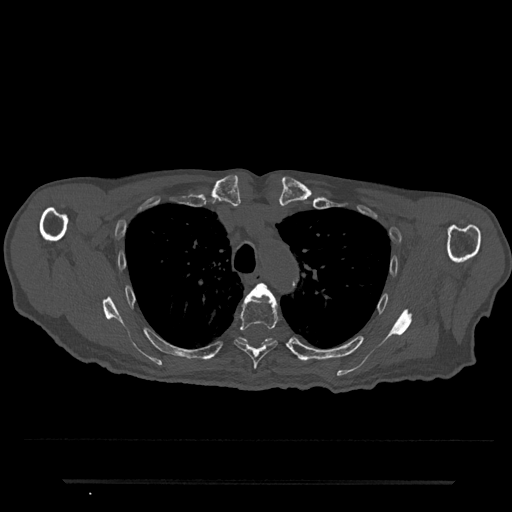
CT including the spine, one axial slice. Bone window (W 1800 / L 400 HU). 0.5 mm slice thickness. 512 × 512 image matrix, field of view 427 × 427 mm. Male patient, age 74 years. Case-level facts recorded for this patient, not image findings: primary cancer: prostate.
Annotated regions visible in this slice (semi-automatically segmented with operator editing):
- T4 vertebra: bounding box [x1, y1, x2, y2] px = [249, 283, 272, 297]
- T5 vertebra: [234, 294, 278, 369]
- T6 vertebra: [238, 338, 272, 344]